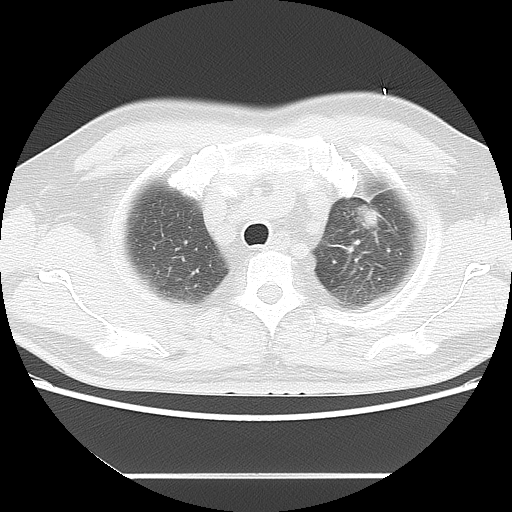
Chest CT, one axial slice. Position 11 of 14 along the scan axis. Reconstruction kernel LUNG. Lung window (W 1500 / L -600 HU). 5 mm slice thickness. 512 × 512 image matrix. Male patient, age 56 years. Case-level facts recorded for this patient, not image findings: clinical TNM (as recorded): T2 N3 M1.
Outlined on this slice (bounding box drawn by a radiologist):
- lung tumour (recorded histology: adenocarcinoma): box from (x=351, y=200) to (x=380, y=238) px